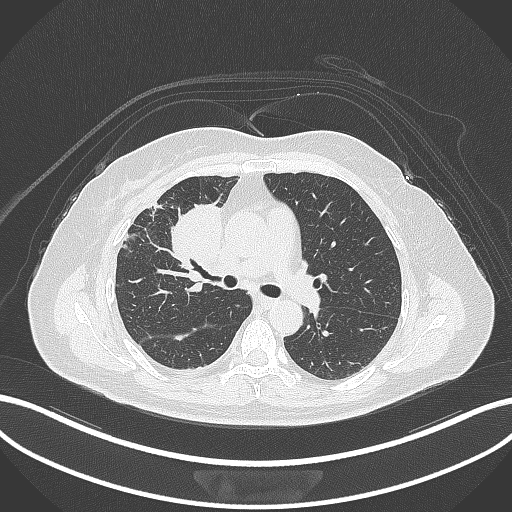
Chest CT, one axial slice. Slice 169 of 305 in the series (ordered by position). 120 kVp. Lung window (W 1500 / L -600 HU). 1 mm slice thickness. 512 × 512 image matrix, field of view 400 × 400 mm. Female patient, age 52 years. From the clinical record (not read from this slice): clinical TNM (as recorded): T3 N1 M1.
Outlined on this slice (bounding box drawn by a radiologist):
- lung tumour (recorded histology: adenocarcinoma): bounding box [x1, y1, x2, y2] px = [165, 201, 226, 278]